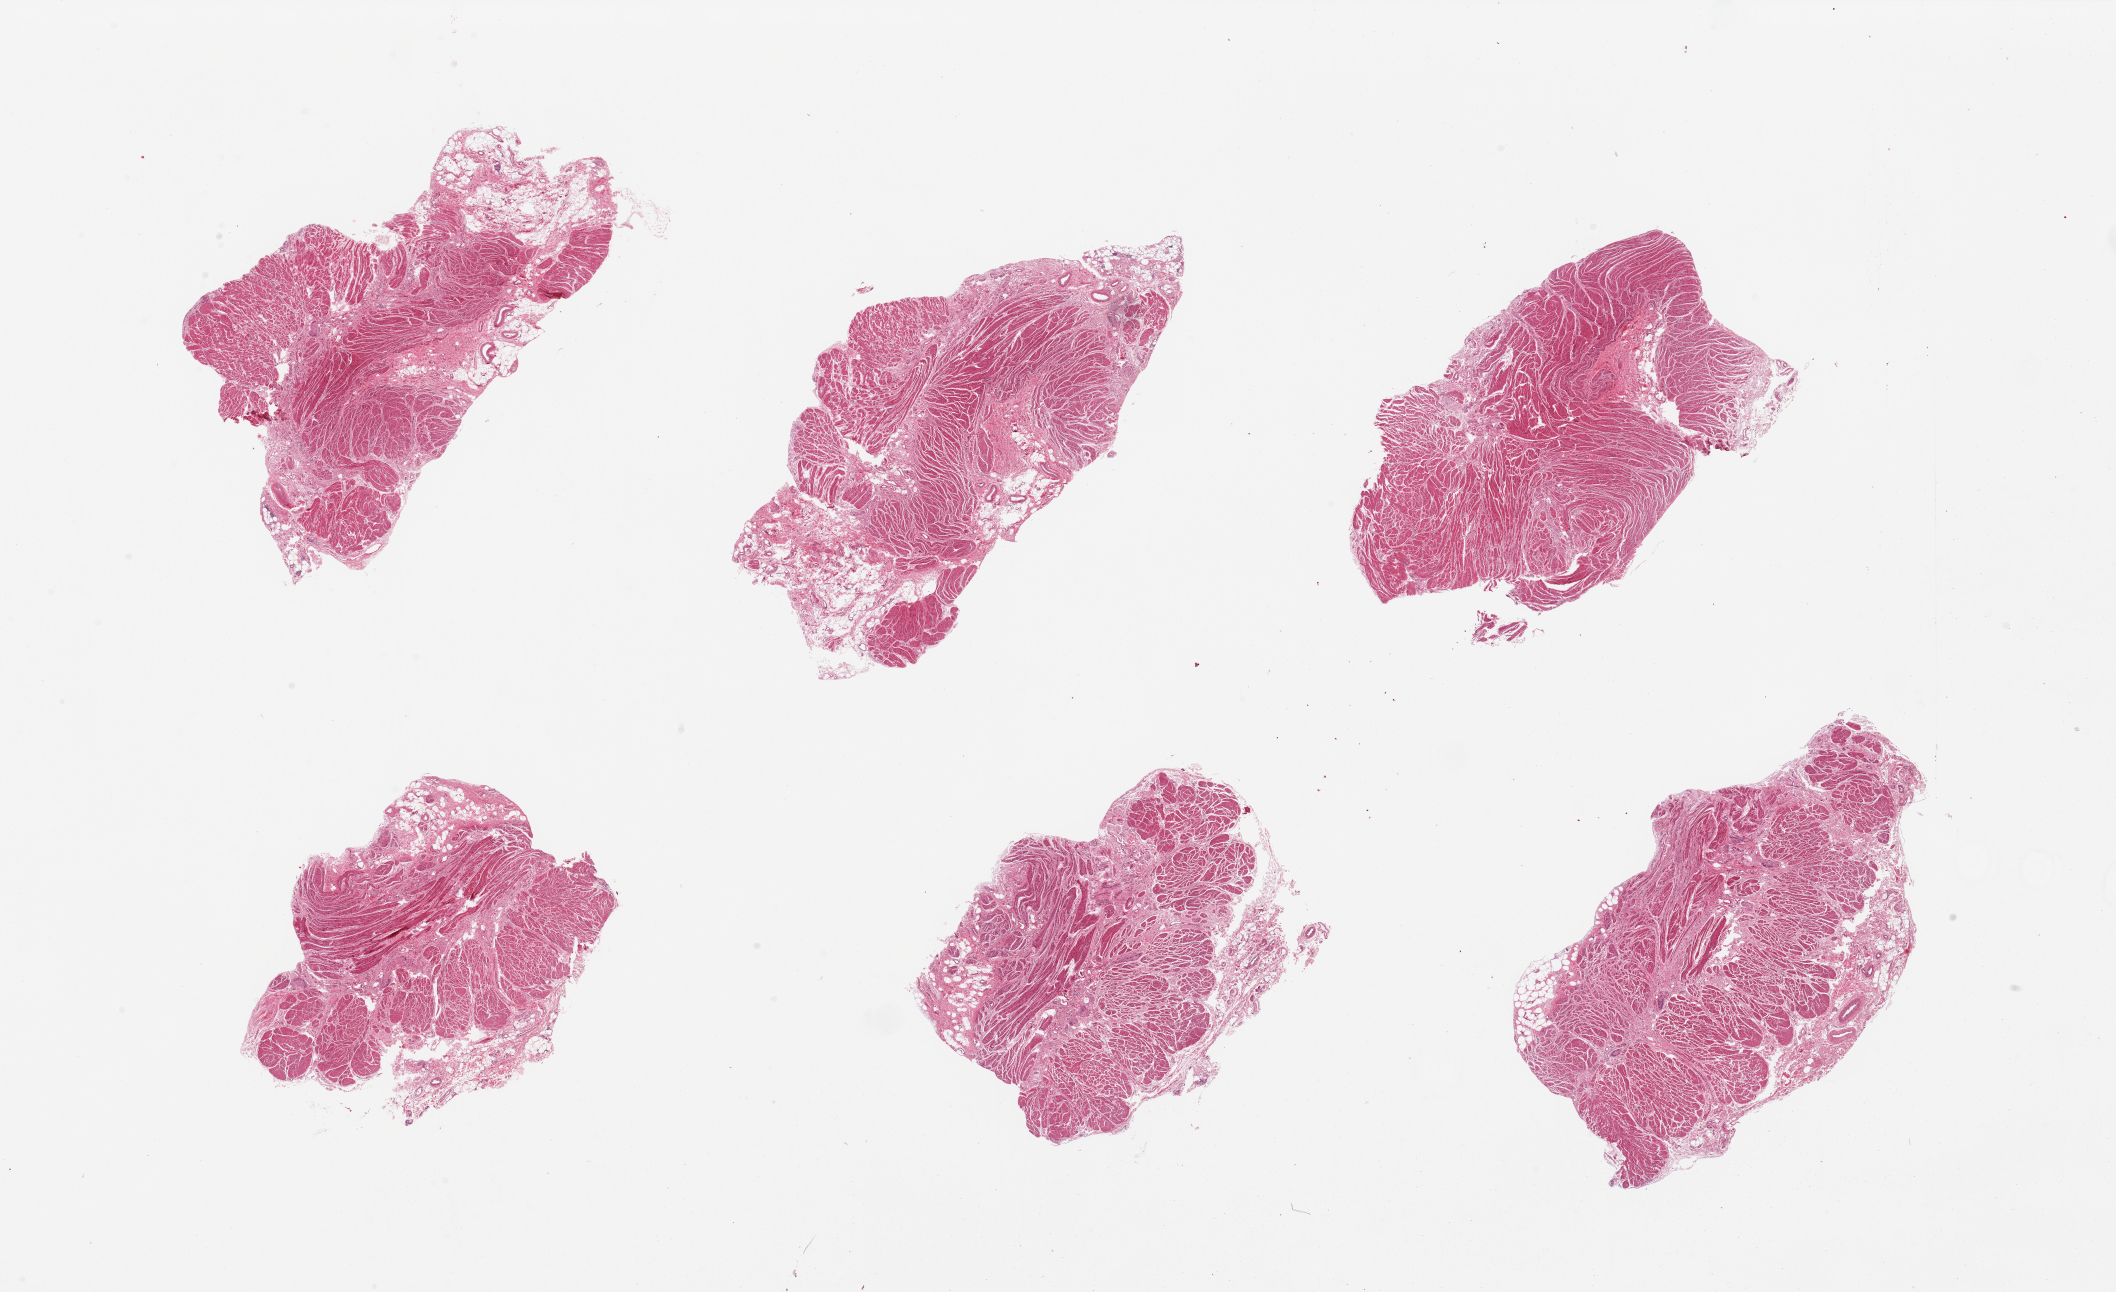
Digitized haematoxylin and eosin-stained section — shown as a low-resolution overview of the whole scanned area (about 33.5 x 20.4 mm). PAXgene-fixed, paraffin-embedded tissue. Sampled site (target tissue): gastroesophageal junction. Tissue donor sample. Female donor.
Reviewer comment on this tissue sample: 6 pieces. Well dissected, 10% internal fat and fibrous tissue.